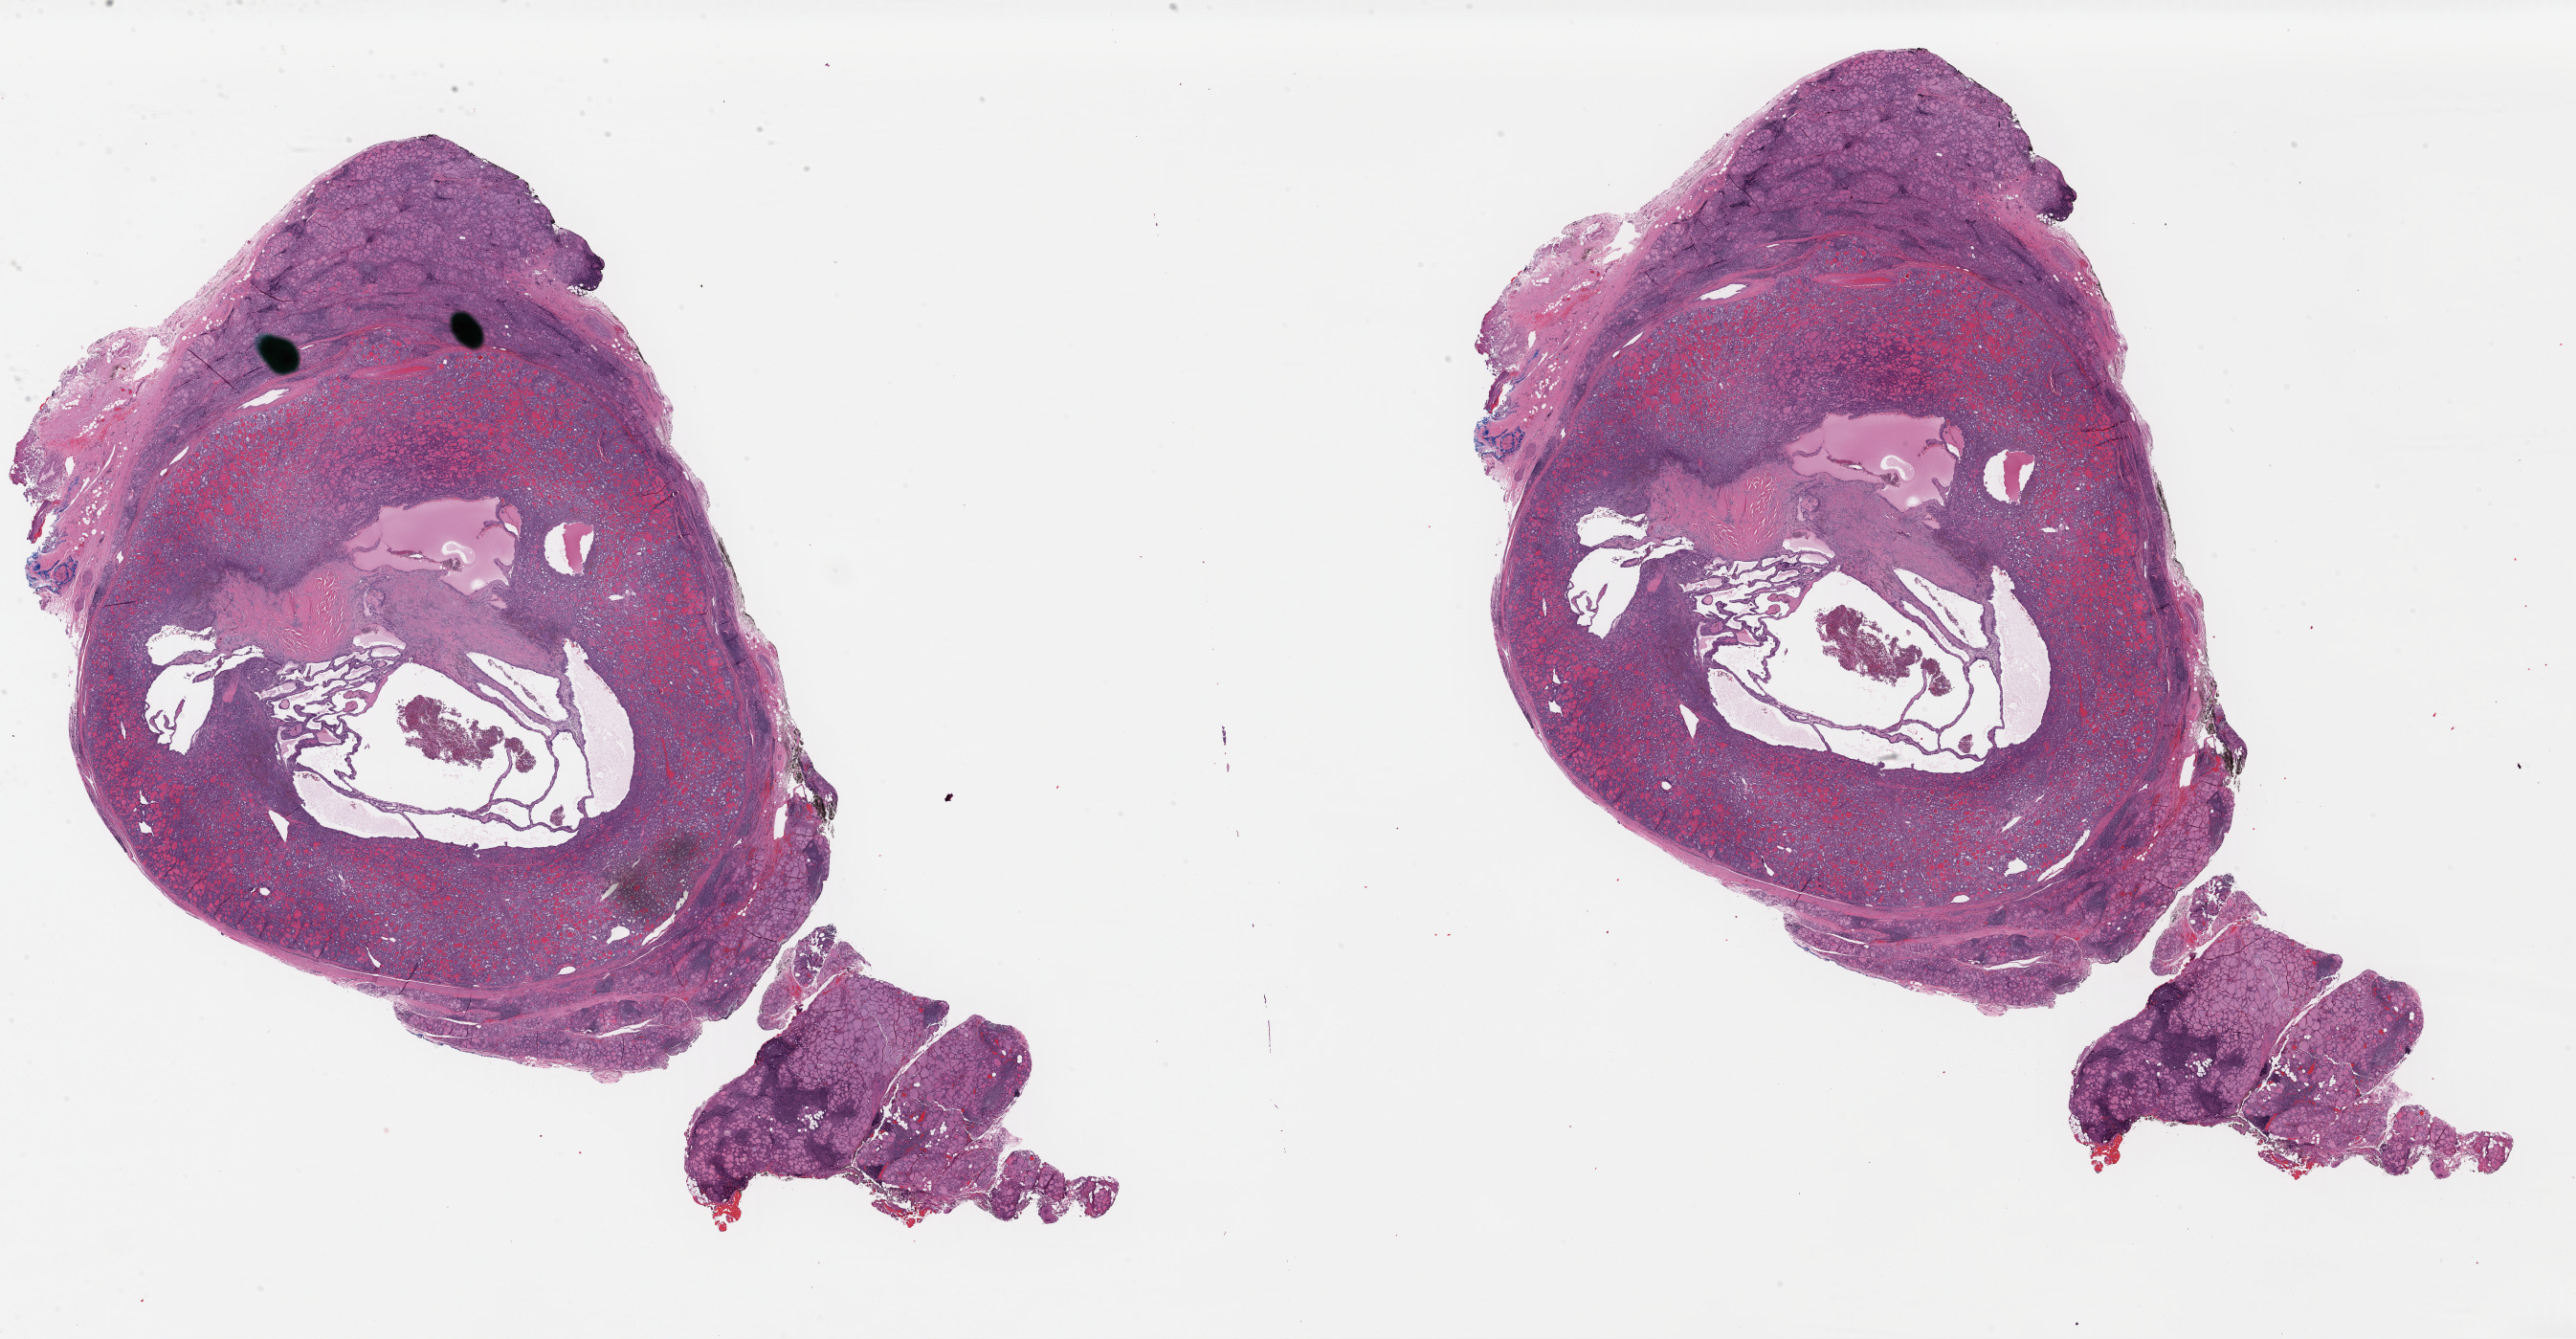
H&E-stained whole-slide image — shown as a low-resolution overview of the whole scanned area (about 42.3 x 22.0 mm, acquisition: 40x scan); formalin-fixed paraffin-embedded (FFPE) diagnostic section; primary tumour sample from the thyroid. Female, age 54 years at initial diagnosis.
AJCC pathologic stage: I (7th edition). Diagnosis: Papillary carcinoma, follicular variant (thyroid gland). TNM: T1b N0 M0. Lymph nodes positive (case pathology): 0 of 4 examined.